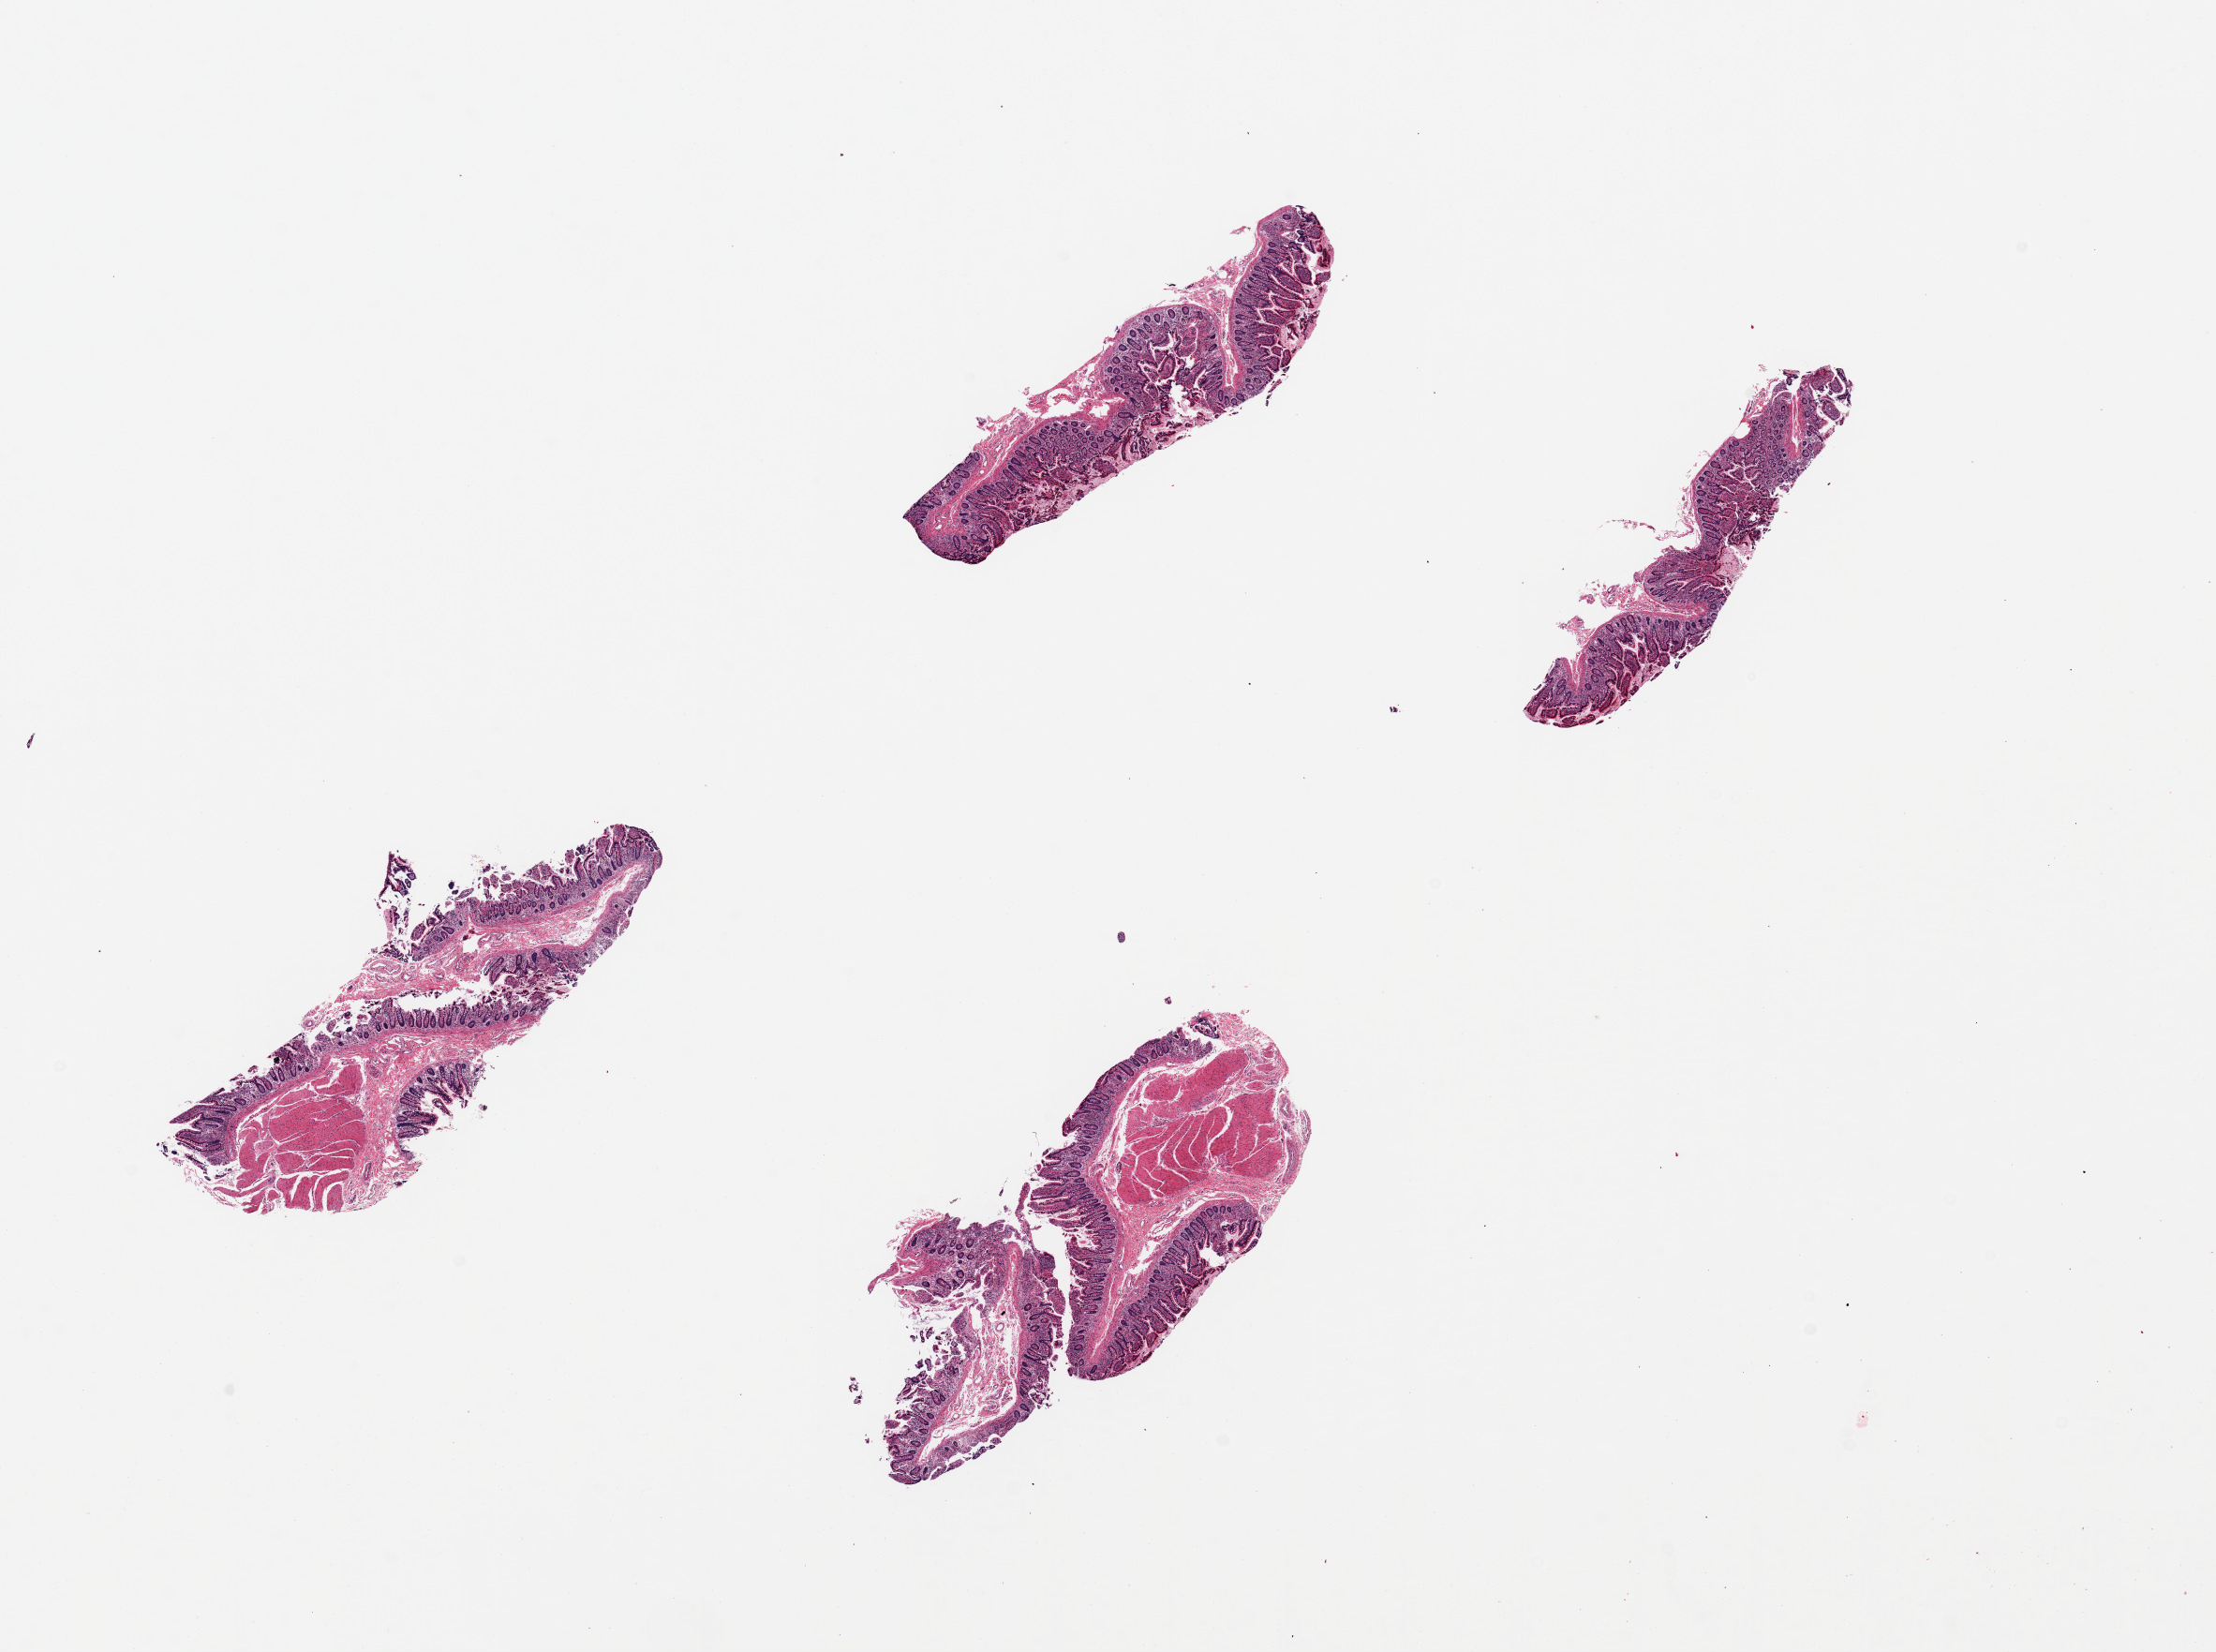
H&E whole-slide image — a low-resolution overview of the entire scanned area, about 18.7 x 13.9 mm, PAXgene-fixed paraffin-embedded (PFPE) section, target tissue: ileum, tissue donor sample. Male donor.
- pathologist's review note for this sample: 4 pieces, up to 5x2mm; mostly mucosa but no lymphoid tissue present